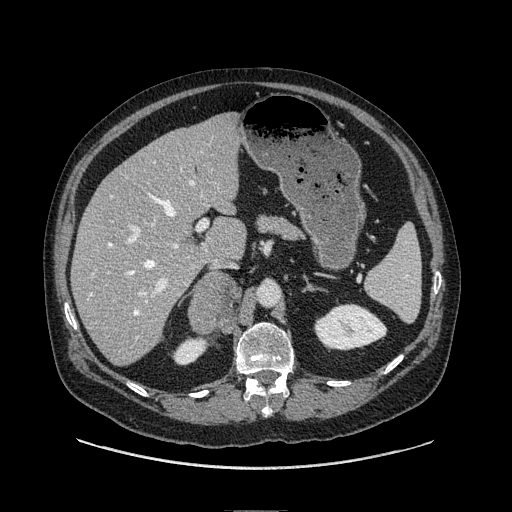
Contrast-enhanced abdominal CT, one axial slice. Position 54 of 149 along the scan axis. Soft-tissue window (W 400 / L 40 HU). 512 × 512 image matrix, field of view 440 × 440 mm. Male patient. From the clinical record (not read from this slice): diagnosis: adrenocortical carcinoma; tumour side: right adrenal; tumour size at pathology: 7.5 cm; Ki-67 index: 15 %; stage (as recorded): 2.
Annotated regions visible in this slice (semi-automatically segmented with operator editing):
- mass: box from (x=188, y=273) to (x=241, y=333) px